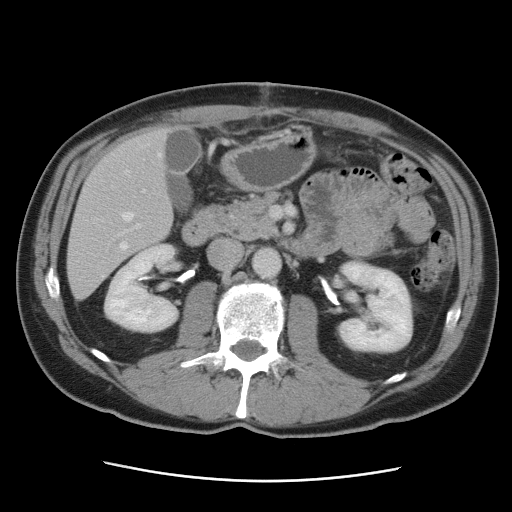
Contrast-enhanced abdominal CT, one axial slice. Slice 37 of 89 in the series (ordered by position). 120 kVp. Intravenous contrast given. Soft-tissue window (W 400 / L 40 HU). 5 mm slice thickness. 512 × 512 image matrix, field of view 366 × 366 mm. Male patient, age 59 years. From the clinical record (not read from this slice): diagnosis: colorectal cancer liver metastases, imaged before liver resection; multiple liver metastases: yes; largest metastasis: 0.6 cm; chemotherapy before resection: no.
Outlined on this slice (outlined manually by an expert reader):
- hepatic veins: bounding box (x1, y1, x2, y2) in pixels: (102, 154, 162, 277)
- liver: (68, 129, 173, 300)
- planned liver remnant (the part of the liver to remain after resection): (74, 128, 173, 245)
- portal vein (with intrahepatic branches): (122, 190, 145, 234)